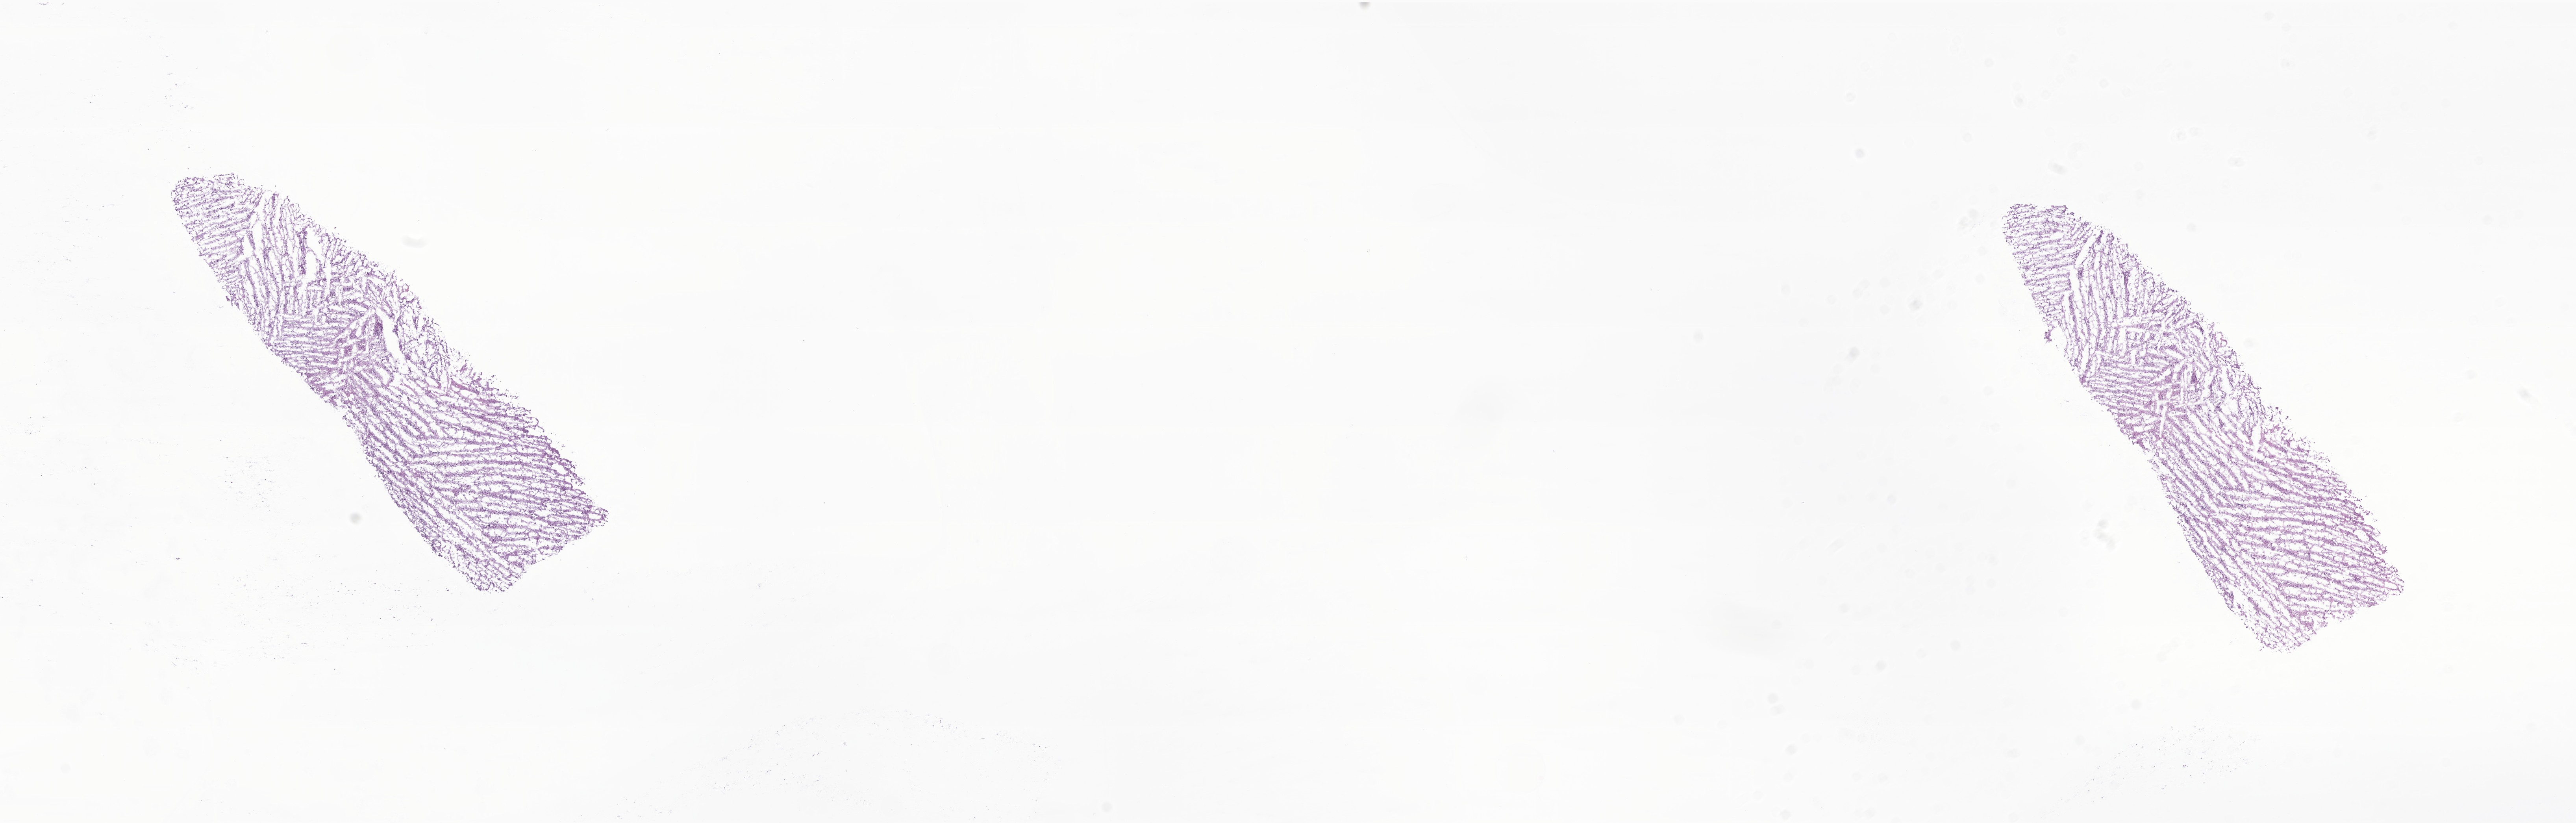
H&E whole-slide image of tumor tissue from the brain — whole scanned area (about 27.6 x 8.8 mm) shown as a low-resolution overview, cryosection (OCT / tissue freezing medium). Patient male; age 189 months (15 years 9 months).
Recorded diagnosis: Neoplasm, uncertain whether benign or malignant.